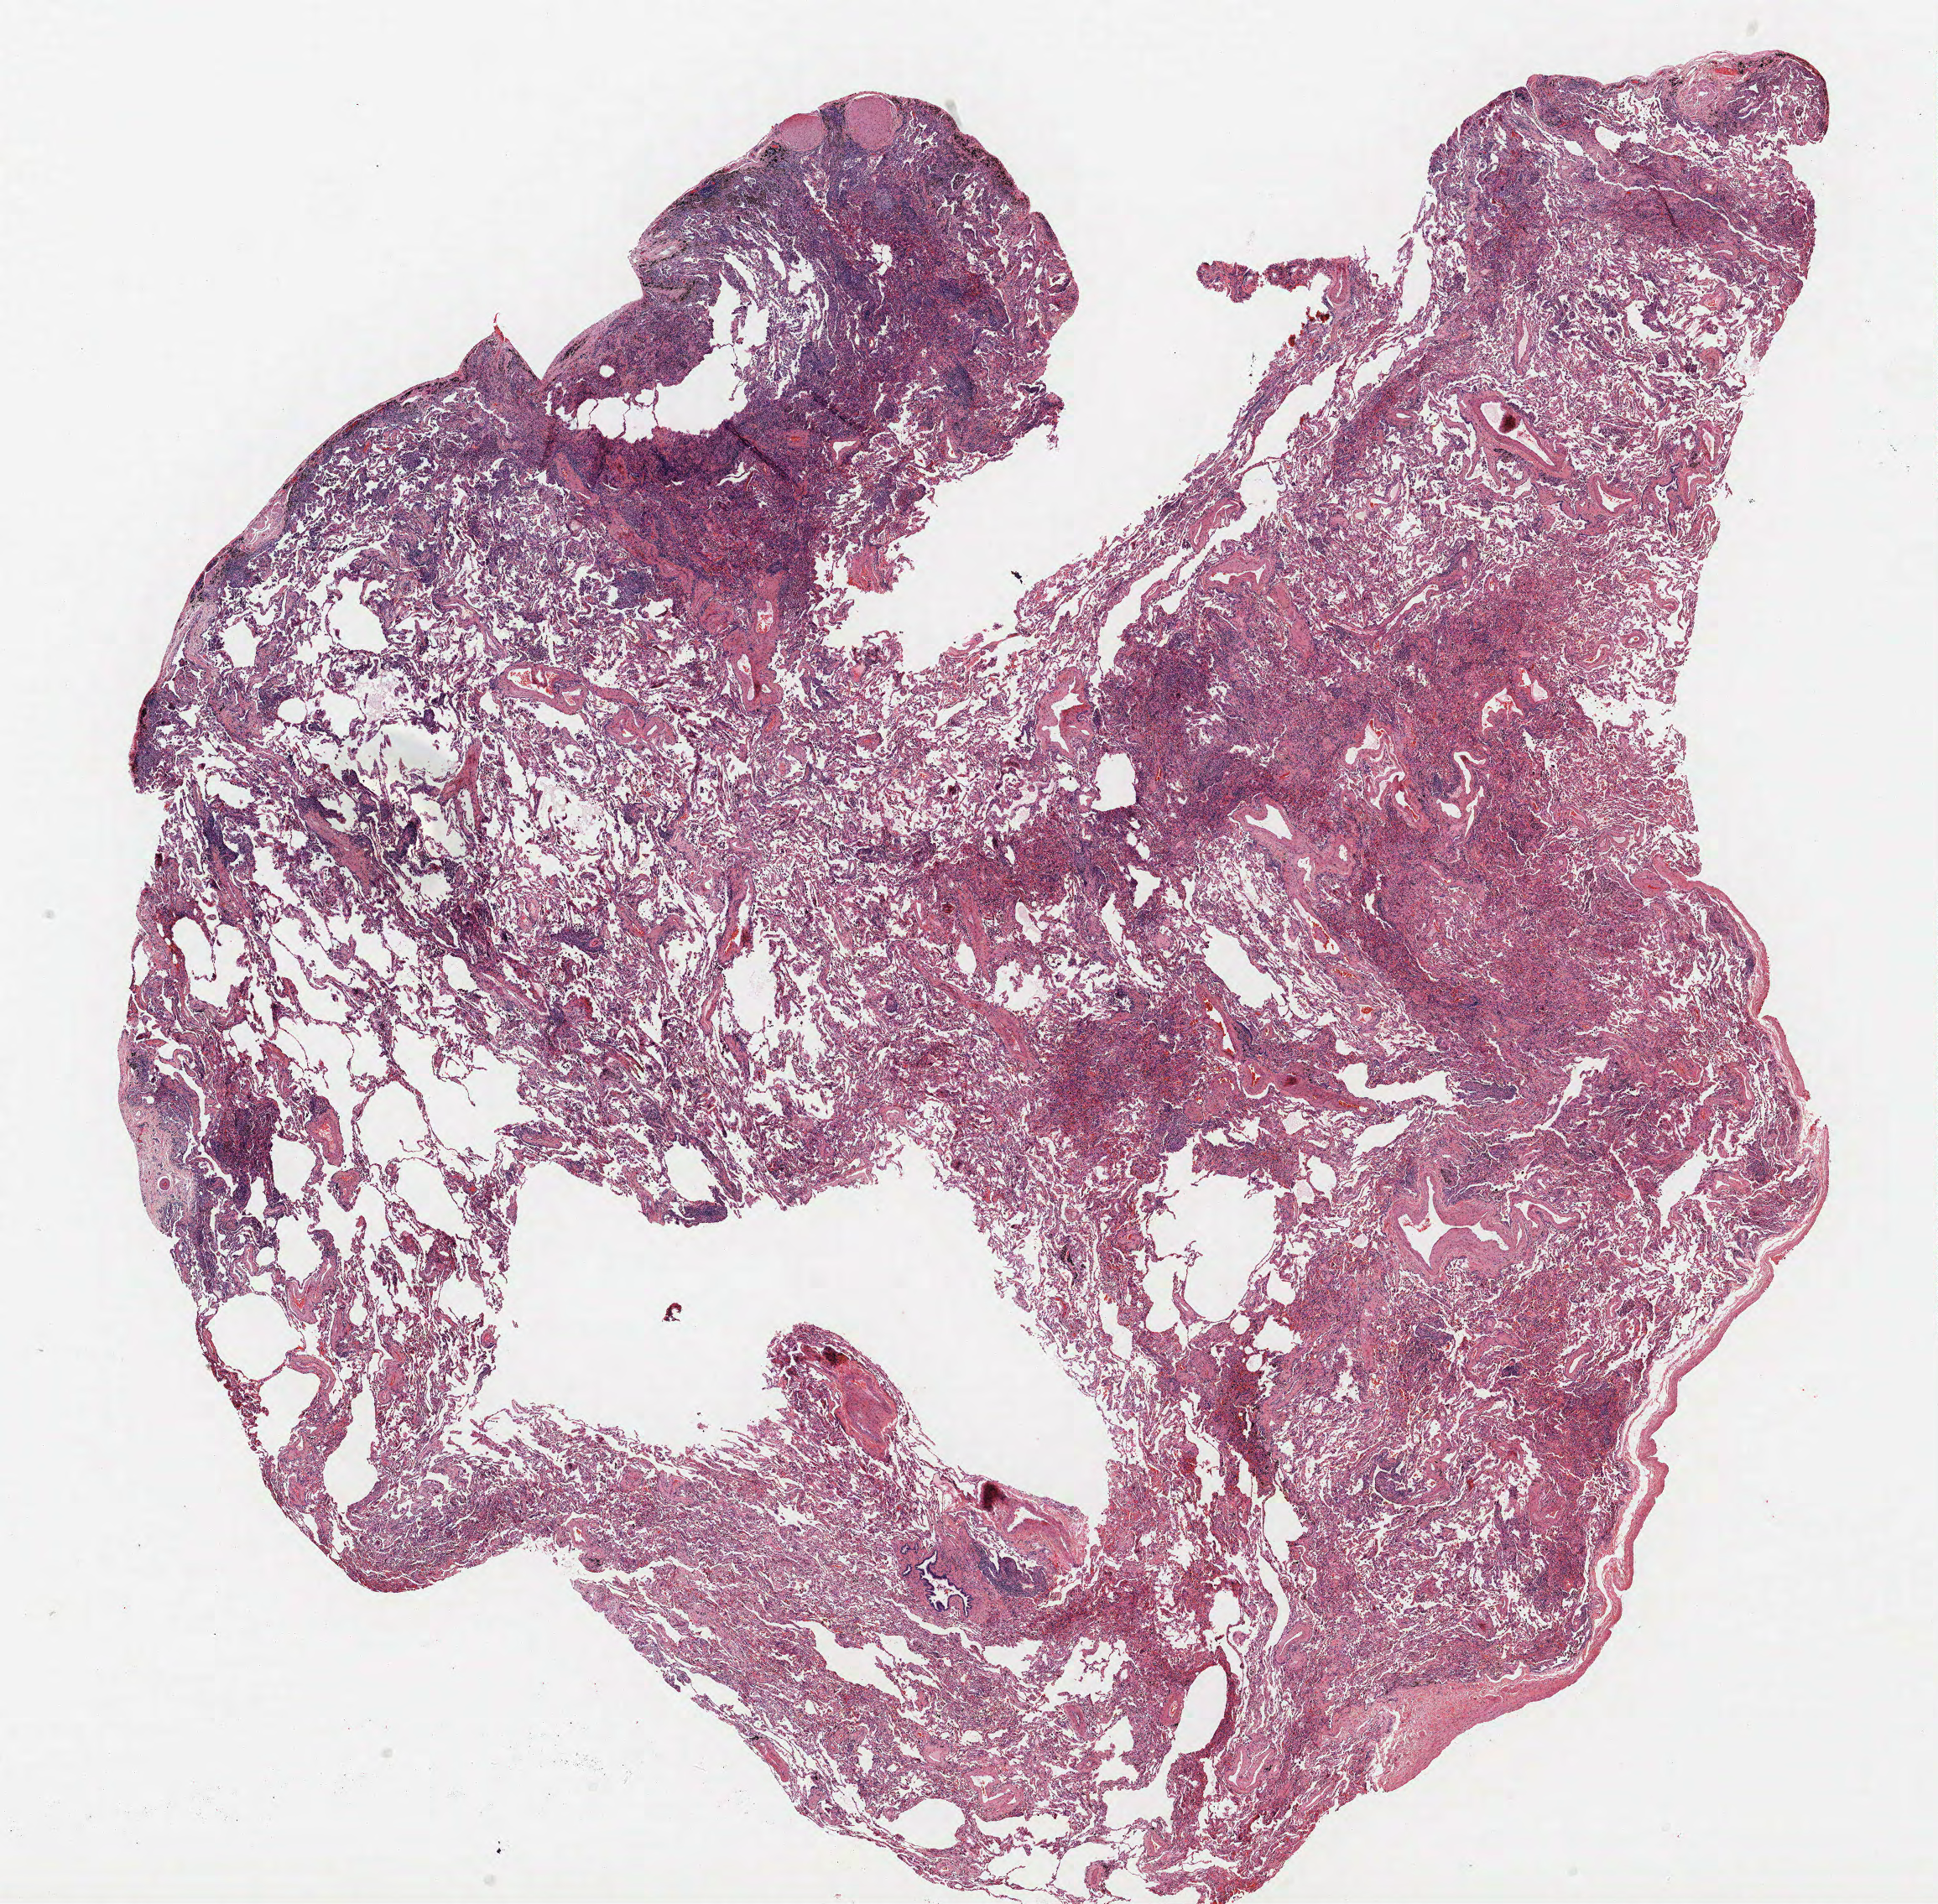
Hematoxylin and eosin (H&E) stained whole-slide image, shown as a low-resolution overview of the whole scanned area (about 18.5 x 18.2 mm, from a 40x scan); formalin-fixed paraffin-embedded (FFPE) section; lung tissue. Male, age 67 at enrolment. Grade: poorly differentiated (G3).
Primary tumour location (clinical record): left upper lobe, left lower lobe. Tumour size (pathology): 18 mm. ICD-O-3 topography: upper lobe of lung (C34.1). Stage (AJCC 6th edition): IIA. Participant's lung-cancer diagnosis: Adenocarcinoma, NOS.